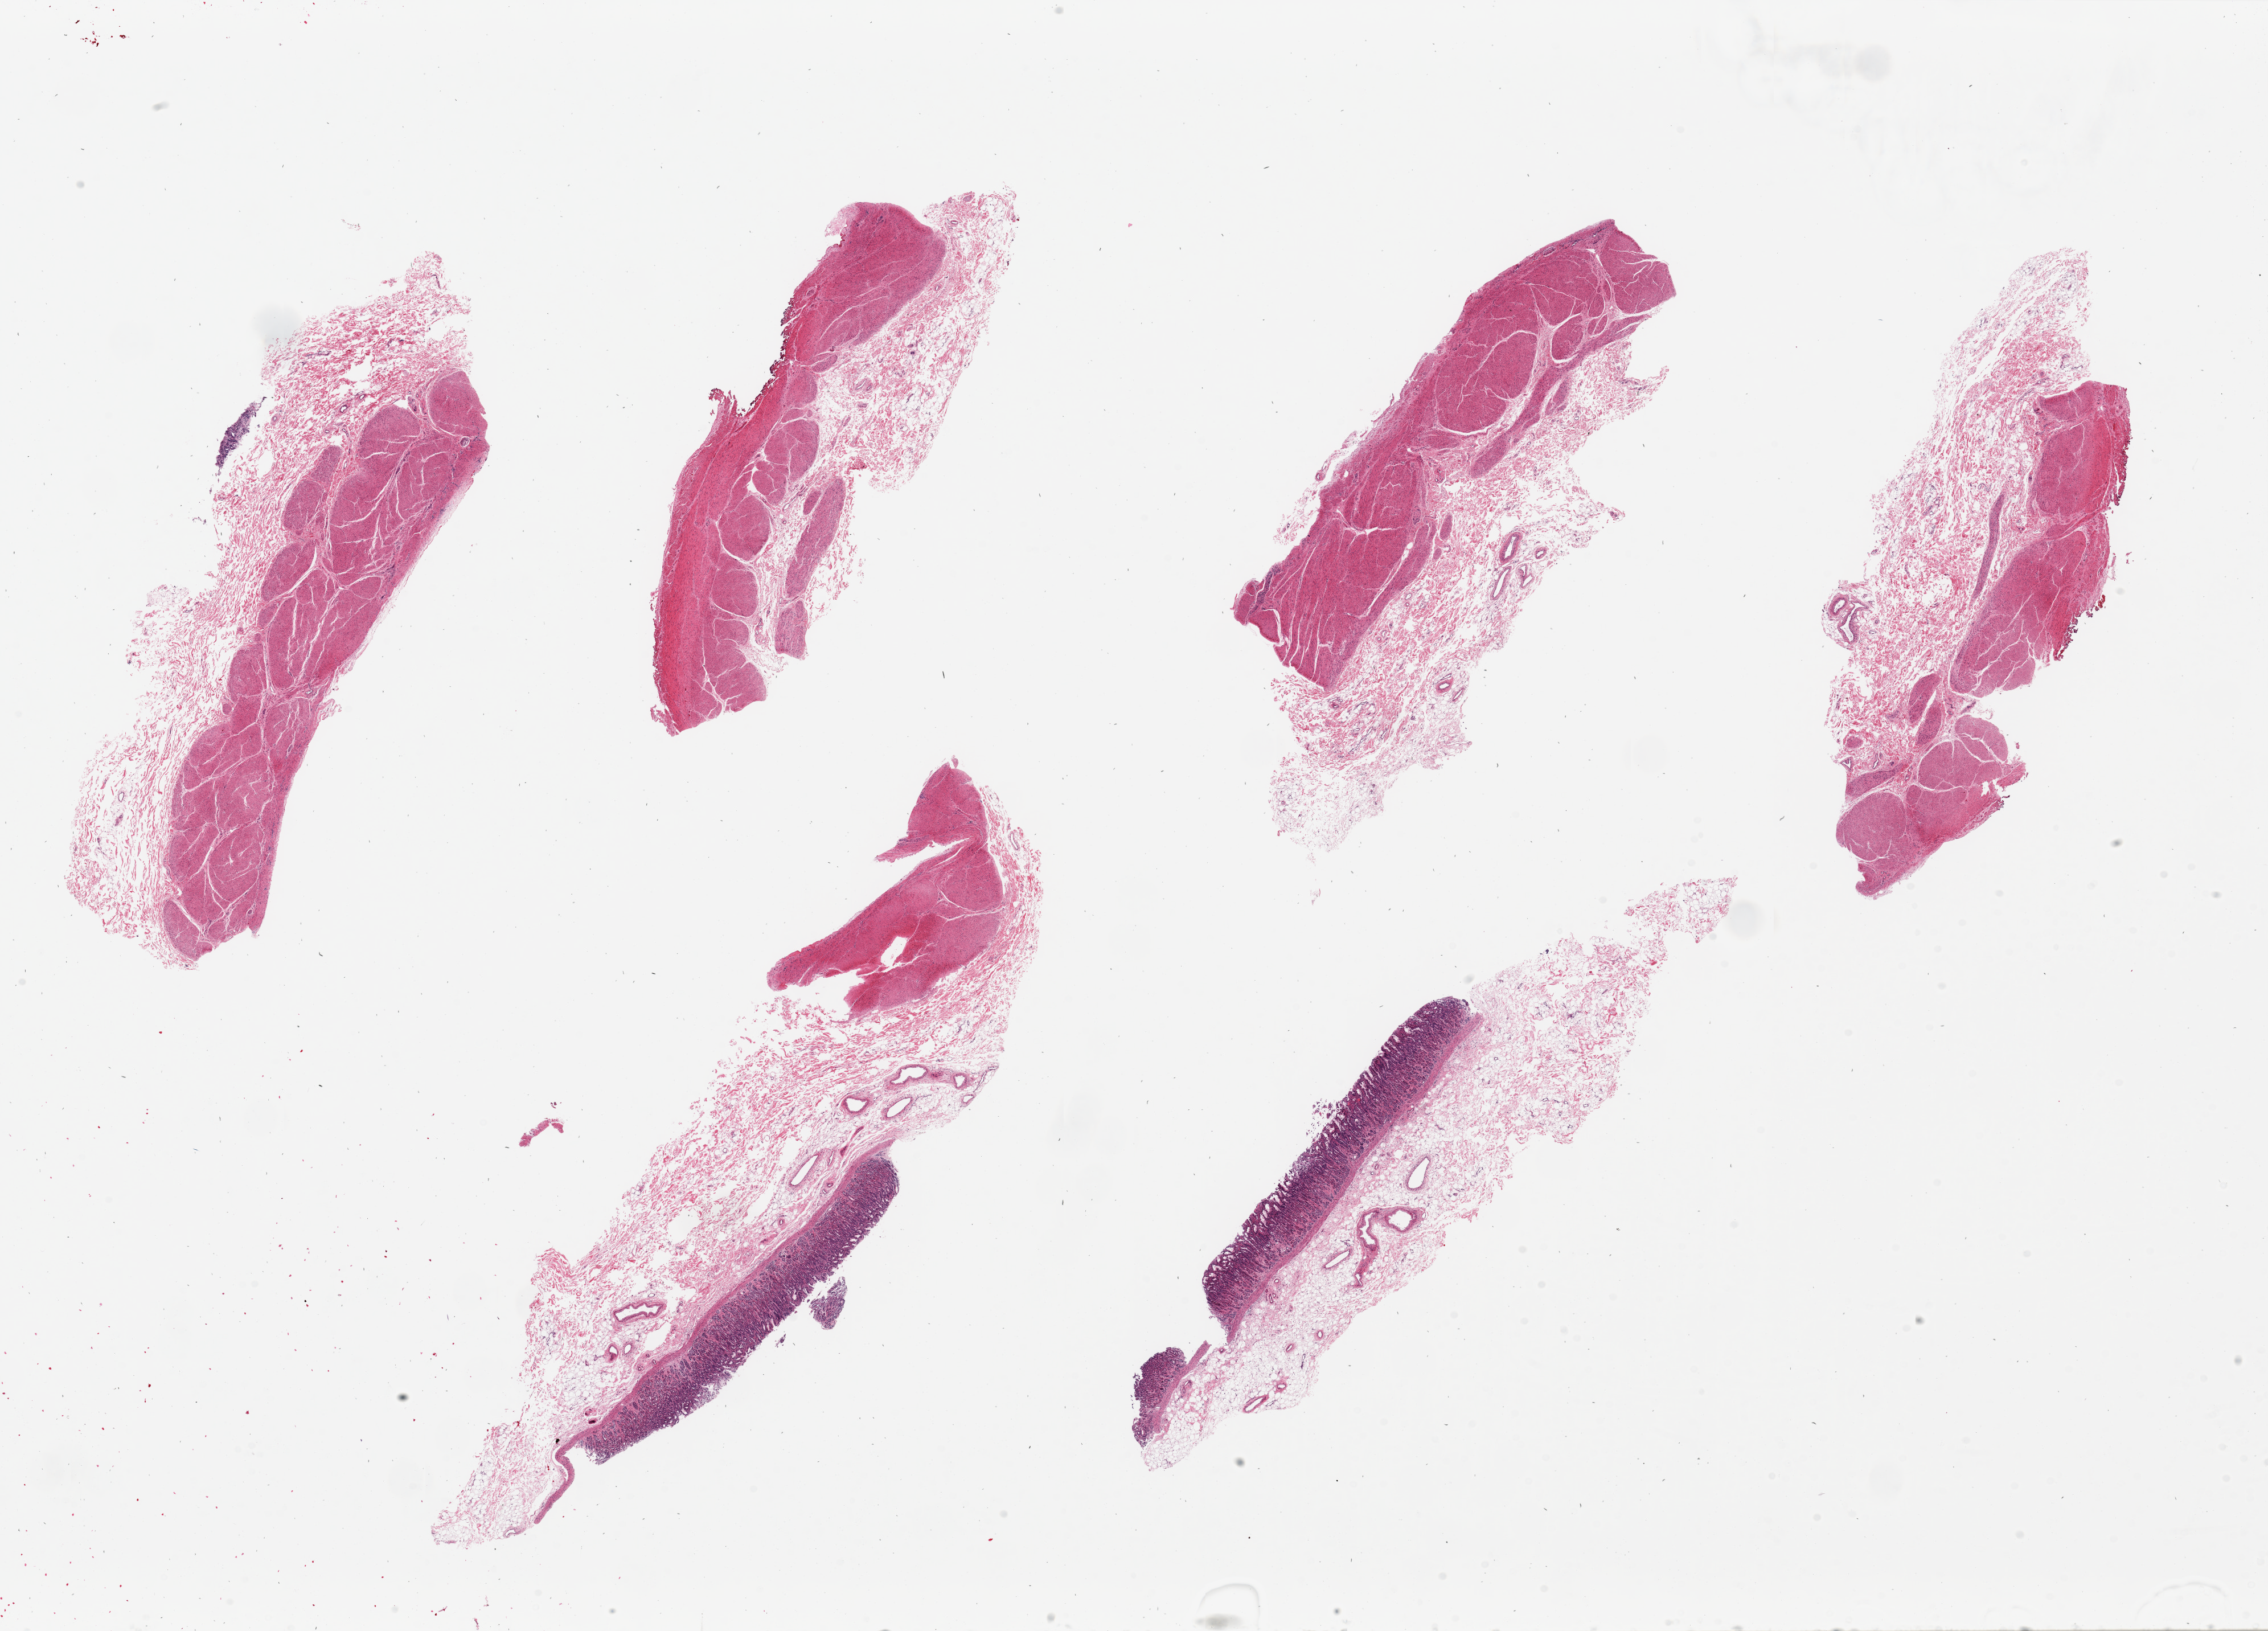
Digitized hematoxylin and eosin (H&E)-stained section, brightfield, shown as a low-resolution overview of the whole scanned area (about 31.5 x 22.7 mm). PAXgene-fixed paraffin-embedded (PFPE) section. Section of stomach (target tissue). Tissue donor sample. Donor: female.
Reviewer comment on this tissue sample: 6 pieces, up to 12x4mm; only 3 have mucosa; one has no muscularis.